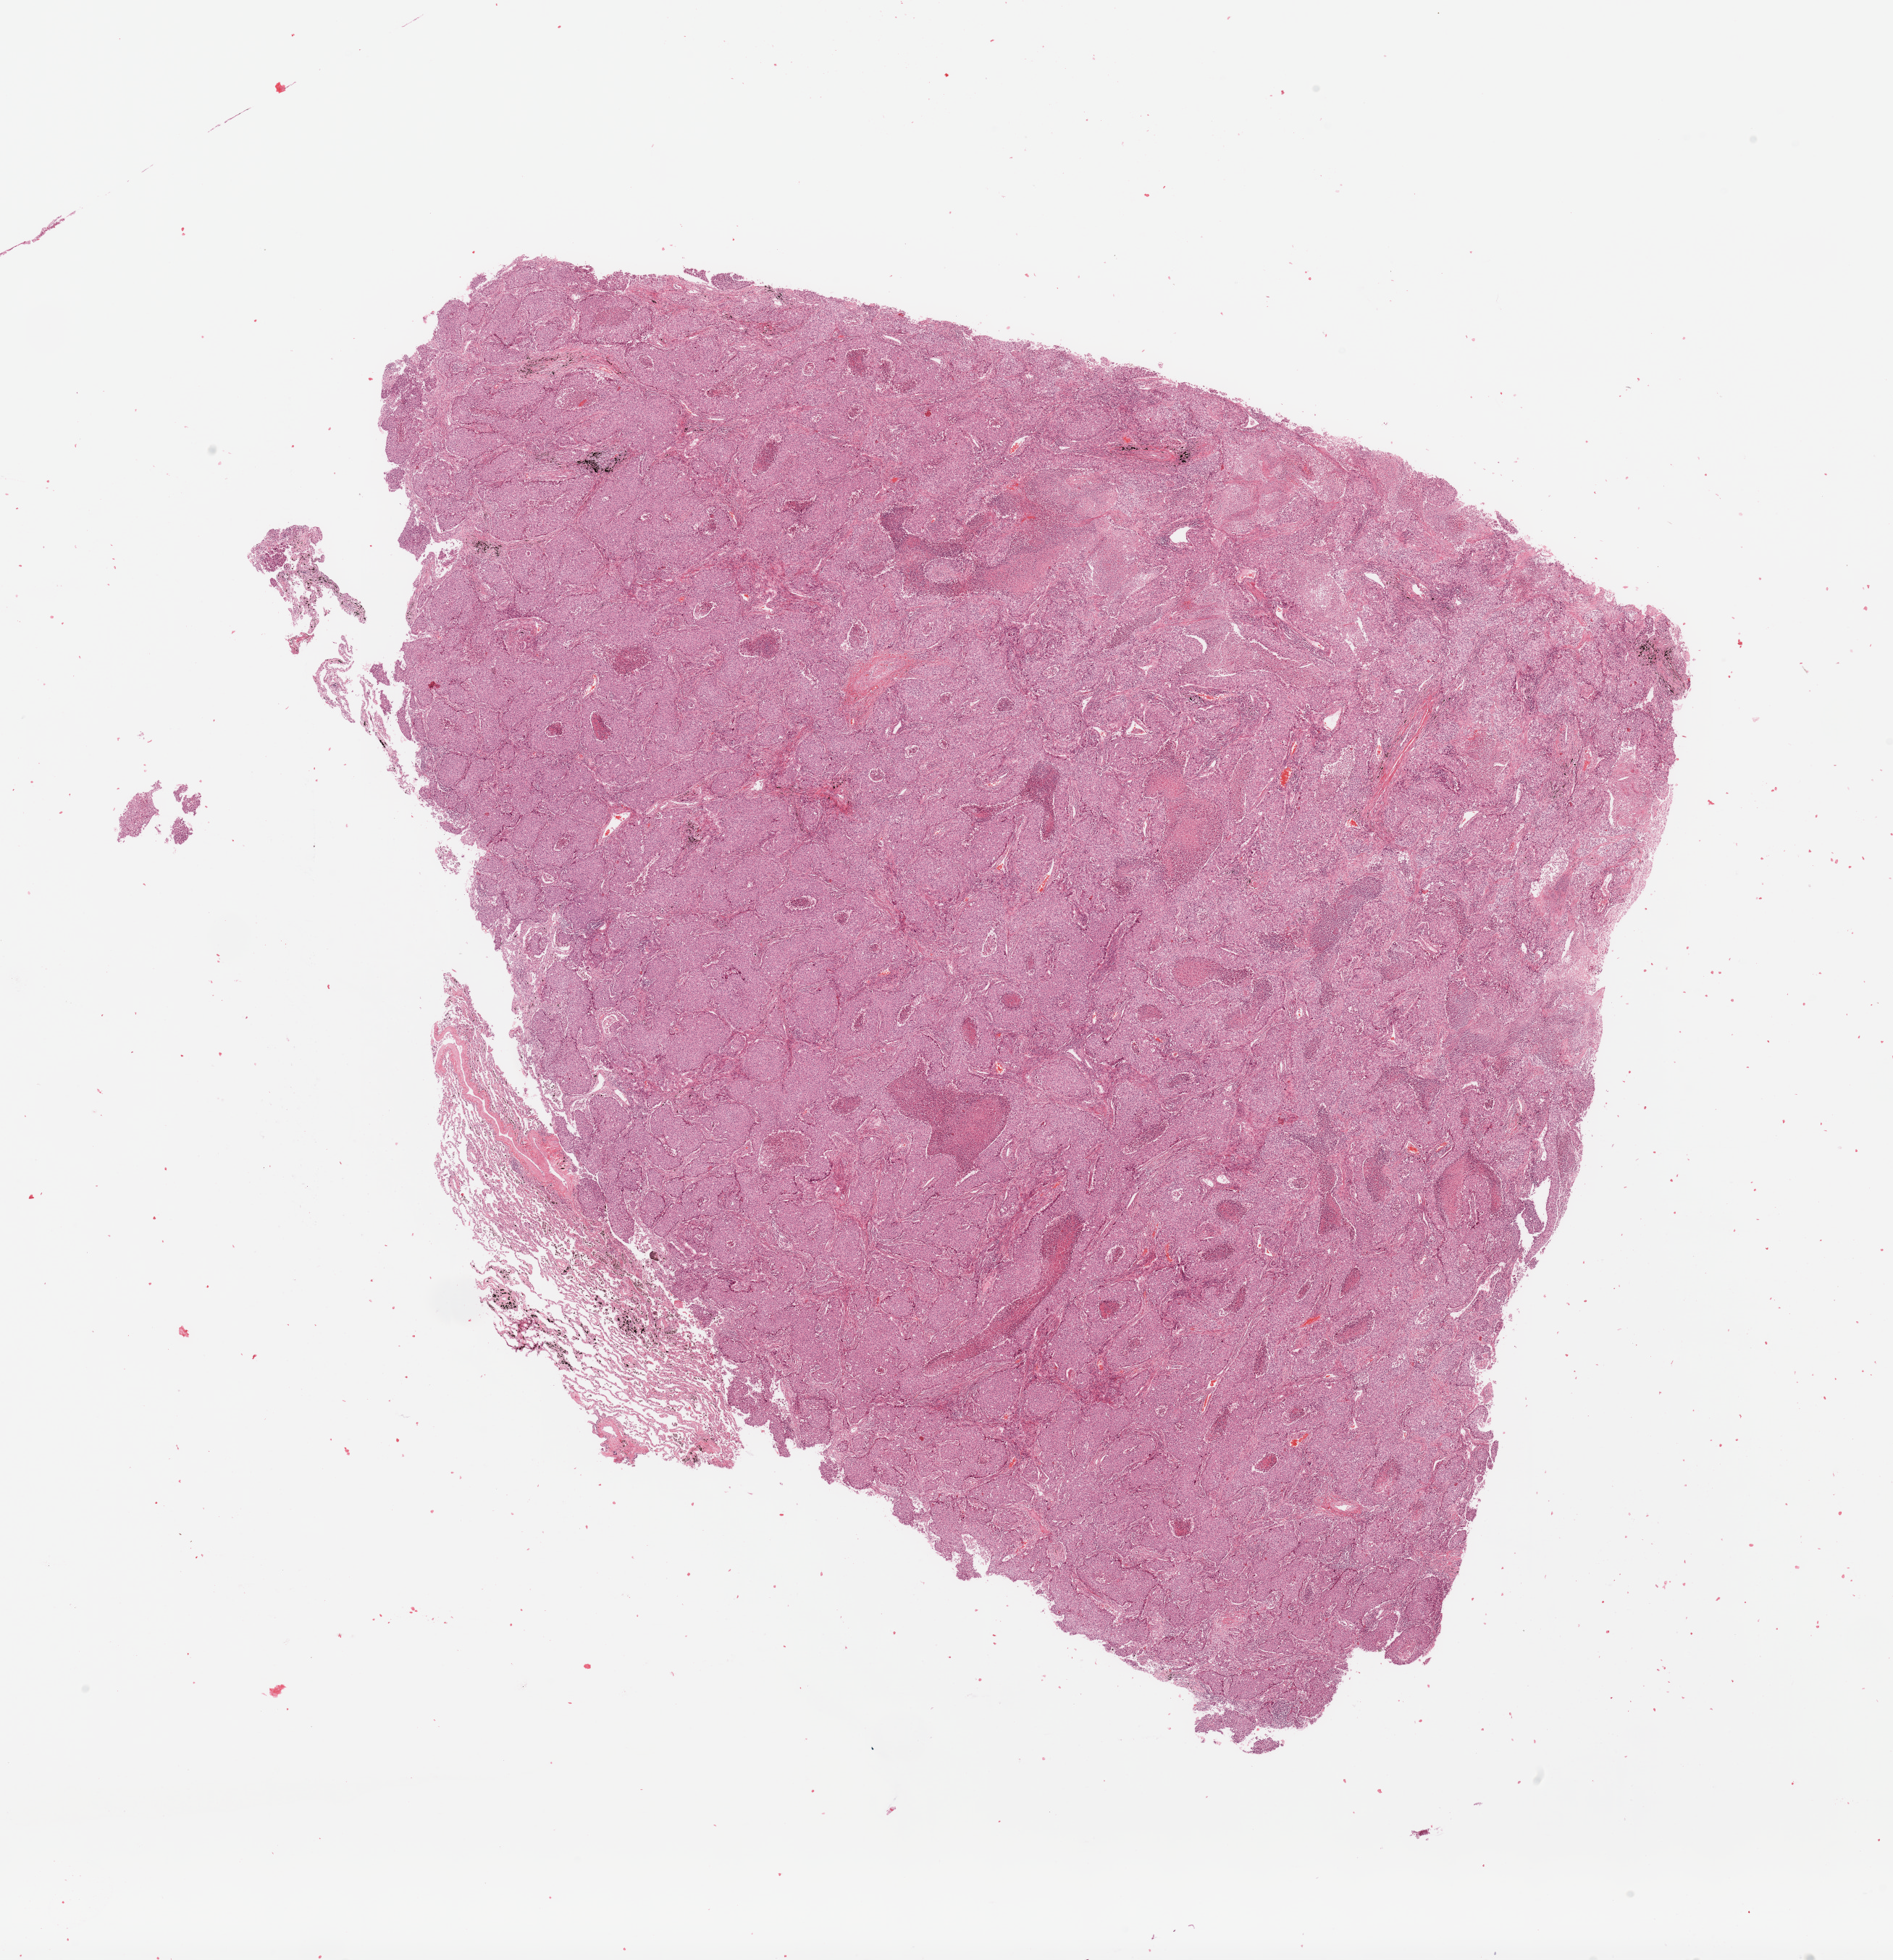
Whole-slide histology image, Hematoxylin and eosin (H&E) stained — shown as a low-resolution overview of the whole scanned area (about 20.7 x 21.4 mm); tumour tissue sample, sampled site: lung. 58-year-old male patient. Histologic grade: G3 (poorly differentiated). Slide review estimates, as recorded: tumour nuclei 80%, necrosis 10%.
* diagnosis: Adenocarcinoma, NOS
* AJCC pathologic stage: IIA